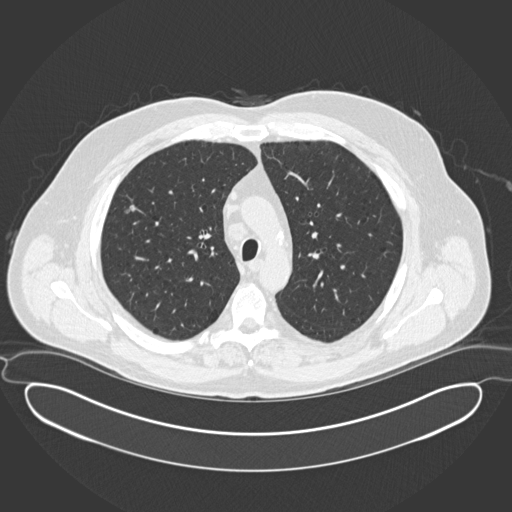
Low-dose screening chest CT, one axial slice; slice 120 of 169 in the series (ordered by position); 120 kVp; lung window (W 1500 / L -600 HU); 512 × 512 image matrix.
Annotated regions visible in this slice (outlined manually by an expert reader):
- lesion 1 (tumor, upper lobe of right lung): bounding box [x1, y1, x2, y2] px = [126, 205, 139, 213]